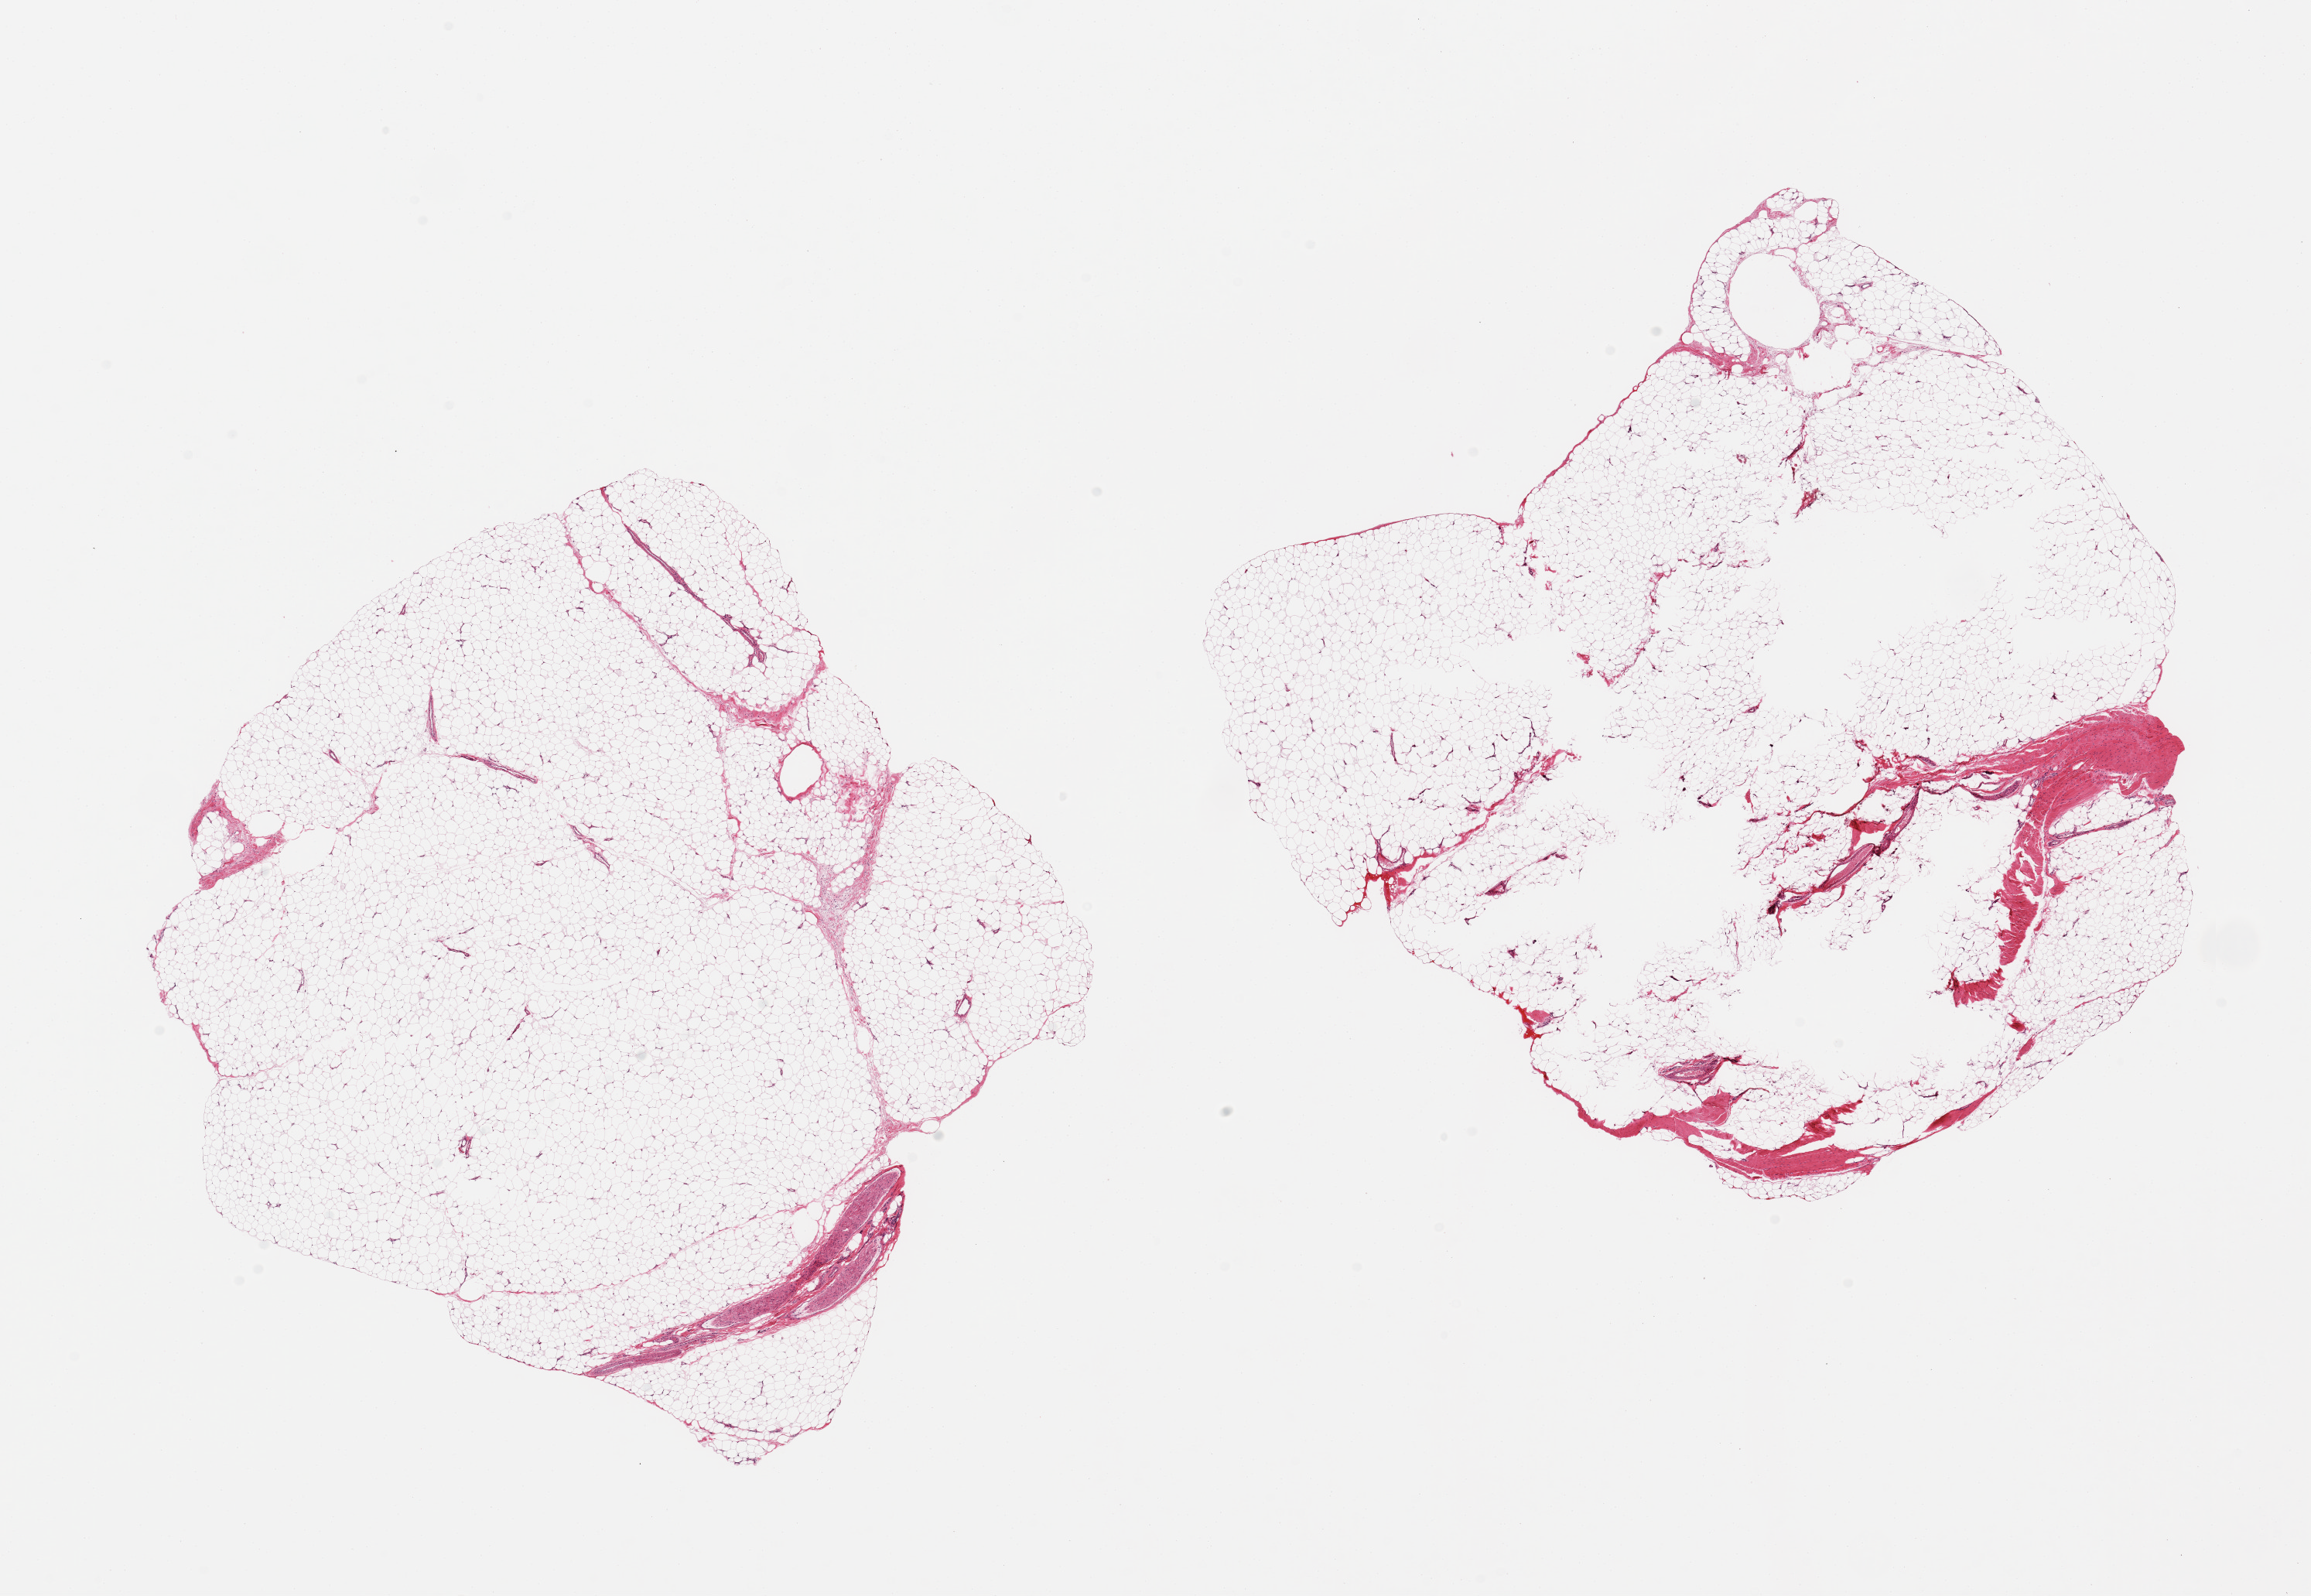
Haematoxylin and eosin whole-slide image, shown as a low-resolution overview of the whole scanned area (about 23.6 x 16.3 mm, slide scanned at 20x). PAXgene-fixed paraffin-embedded (PFPE) section. Section of adipose tissue (target tissue). Tissue donor sample. Donor: male.
Review note (as recorded): 2 pieces; 5% fibrous content.